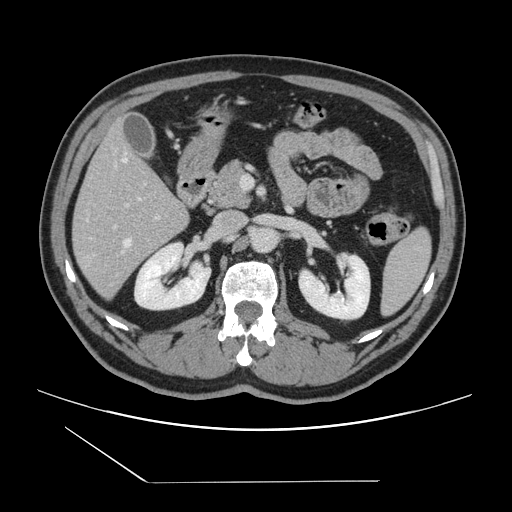
Contrast-enhanced abdominal CT, one axial slice; slice 67 of 157 in the series (ordered by position); soft-tissue window (W 400 / L 40 HU); 2.5 mm slice thickness; 512 × 512 image matrix, field of view 407 × 407 mm. Male patient, age 61 years. From the clinical record (not read from this slice): diagnosis: colorectal cancer liver metastases, imaged before liver resection; multiple liver metastases: yes; largest metastasis: 5.5 cm; disease in both lobes: yes.
Structures marked on this image (outlined manually by an expert reader):
- hepatic veins: bounding box (x1, y1, x2, y2) in pixels: (123, 156, 140, 251)
- liver: (74, 126, 188, 298)
- planned liver remnant (the part of the liver to remain after resection): (75, 125, 177, 218)
- portal vein (with intrahepatic branches): (114, 166, 160, 228)